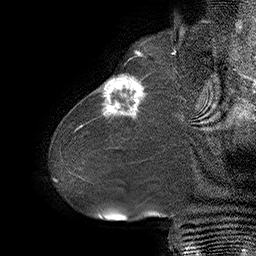
Breast MRI (dynamic contrast-enhanced), one sagittal slice. Position 12 of 55 along the scan axis. Dynamic contrast-enhanced series, time point 2 of 6 at this slice position (early post-contrast). 1.5 T. TE 4.5 ms, TR 32.4 ms. 256 × 256 image matrix, field of view 180 × 180 mm. Female patient. Case-level facts recorded for this patient, not image findings: setting: breast cancer imaged before/during neoadjuvant chemotherapy; receptor status: HER2-positive.
Outlined on this slice (semi-automatically segmented with operator editing):
- analysis volume of interest (the breast-tissue region the enhancement analysis was run in; not a lesion): bounding box <80,64,163,134> (left, top, right, bottom; pixels)
- tumour enhancement mask (voxels above the 100 % enhancement threshold inside the analysis volume of interest): <80,76,145,128>